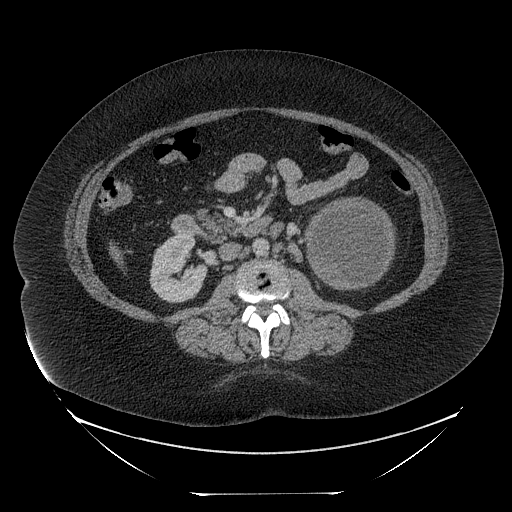
Contrast-enhanced abdominal CT, one axial slice; slice 117 of 205 in the series (ordered by position); 120 kVp; intravenous contrast given; soft-tissue window (W 400 / L 40 HU); 512 × 512 image matrix, field of view 500 × 500 mm. Patient: female, 53 years. From the clinical record (not read from this slice): diagnosis: adrenocortical carcinoma; tumour side: left adrenal; tumour size at pathology: 17 cm; Ki-67 index: 20 %; stage (as recorded): 3.
Structures marked on this image (semi-automatically segmented with operator editing):
- mass: box from (x=309, y=199) to (x=393, y=287) px